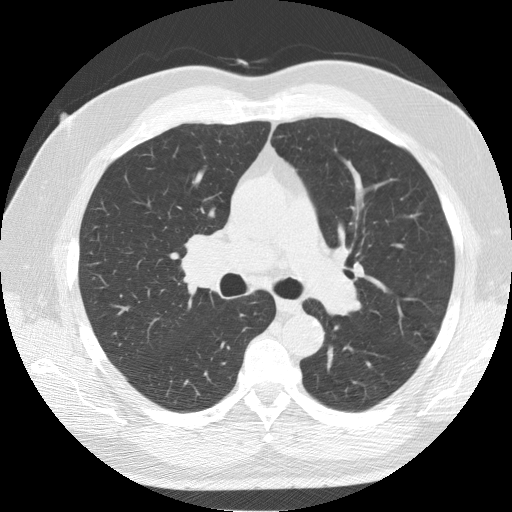
Chest CT (low-dose screening protocol), one axial image. Second screening round (one year after baseline). Lung window (W 1500 / L -600 HU). 2.5 mm slice thickness. Slice 52 of 139 in the series. Male participant, aged 64 years at enrolment. Former smoker at enrolment.
- Expert reader's lesion annotation, box from (x=166, y=222) to (x=259, y=303) px.
- Reader record for this screening exam (exam-level; its link to the box is not recorded): non-calcified nodule or mass ≥4 mm, right lower lobe, 7 × 5 mm, smooth margins, soft tissue attenuation, pre-existing on the prior screen: yes; interval growth: no.
- Later outcome: lung cancer diagnosed 63 days after this screen — adenocarcinoma, NOS, right upper lobe, poorly differentiated (G3), stage IB (AJCC 6th edition), 37 mm at pathology.